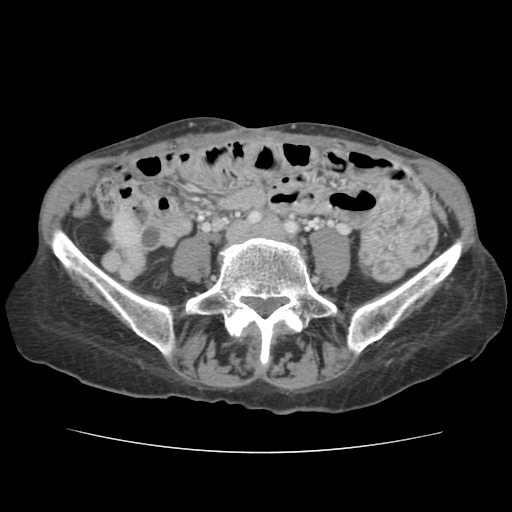
Contrast-enhanced abdominal CT, one axial slice. 120 kVp. Soft-tissue window (W 400 / L 40 HU). 2.5 mm slice thickness. 512 × 512 image matrix, field of view 319 × 319 mm. Female patient, age 77 years. From the clinical record (not read from this slice): diagnosis: colorectal cancer liver metastases, imaged before liver resection; multiple liver metastases: yes; largest metastasis: 3 cm; disease in both lobes: no.
Structures marked on this image (outlined manually by an expert reader):
- liver: bounding box (x1, y1, x2, y2) in pixels: (115, 214, 137, 245)